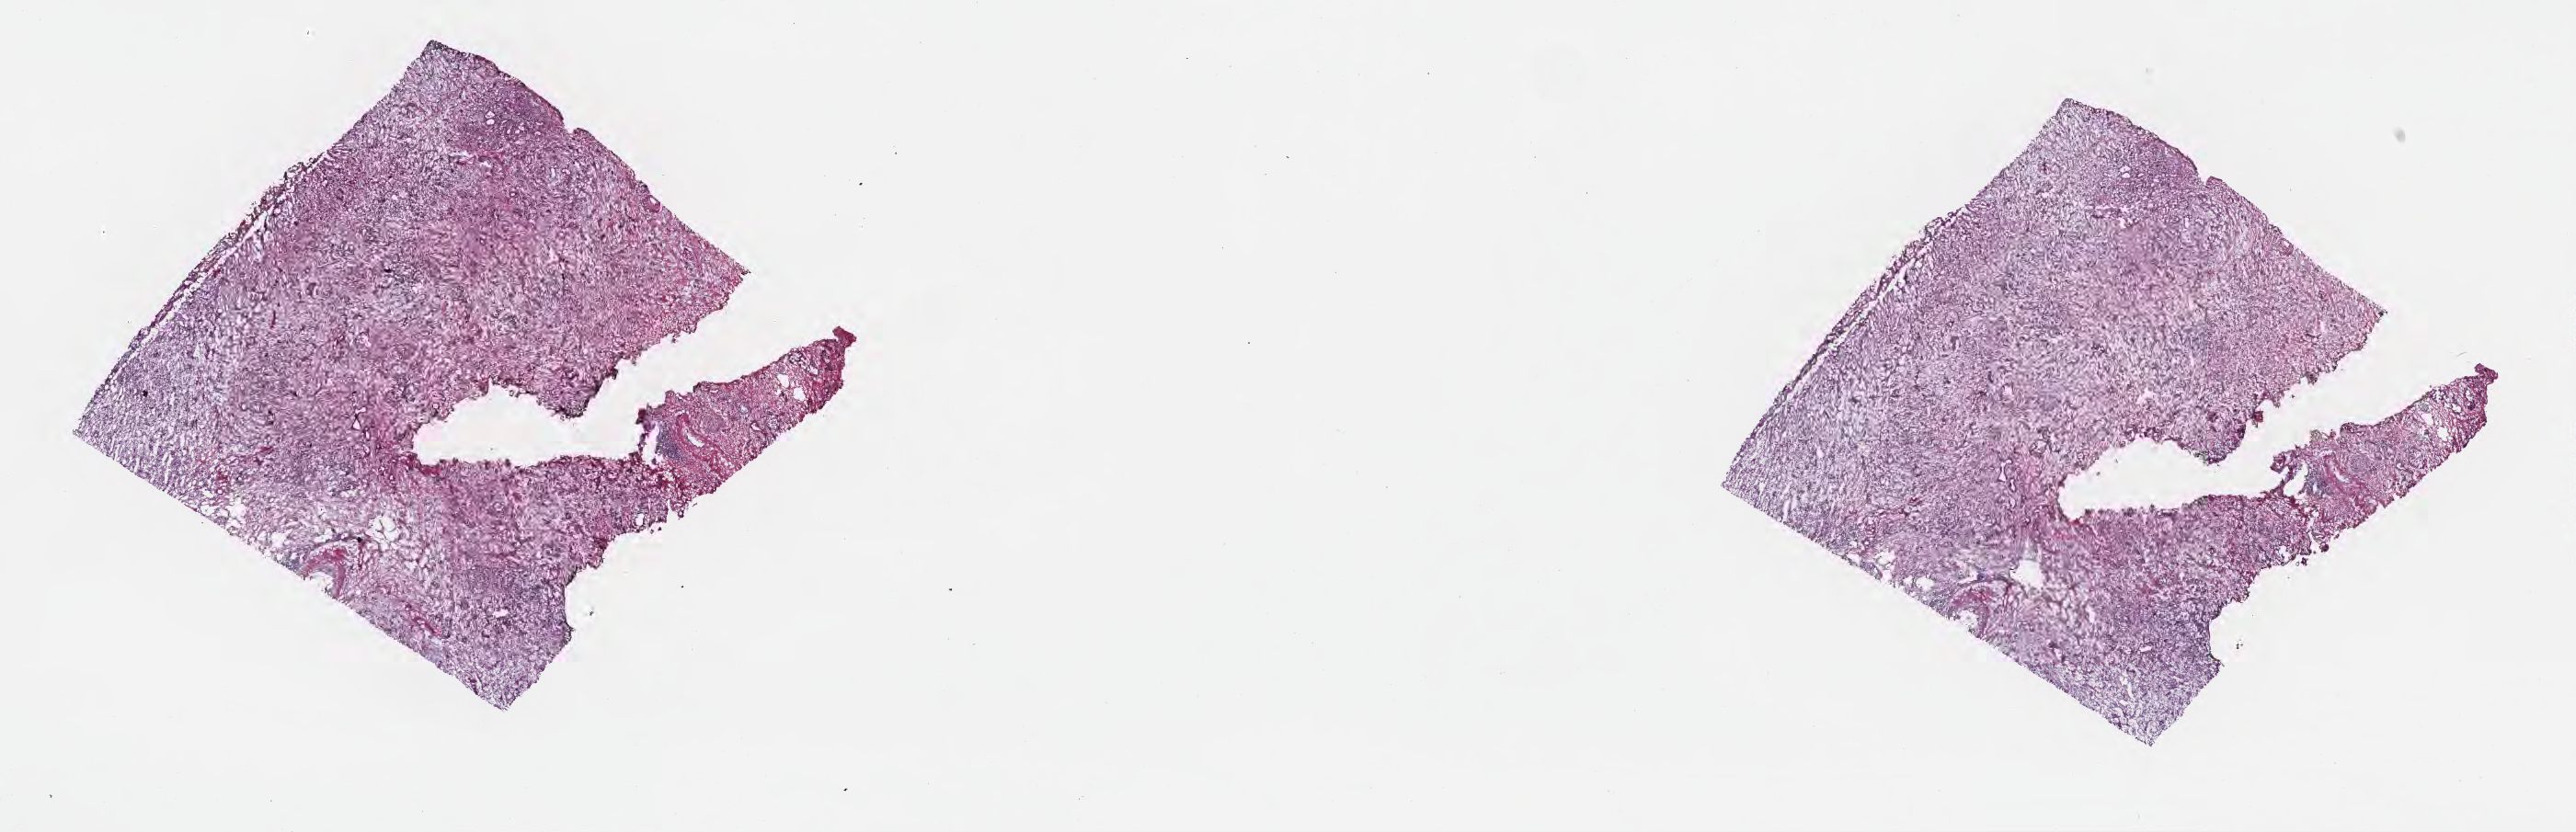
H&E whole-slide image — a low-resolution overview of the entire scanned area, about 22.7 x 7.3 mm, frozen section (tissue freezing medium), primary tumor, site: head of pancreas. Male, age 75 years at initial diagnosis. Tumor grade: G2 (moderately differentiated). Pathologist review of this section (percent, as recorded): tumor cells 15%, tumor nuclei 80%, stromal cells 85%, necrosis 0%, normal cells 0%. Infiltration values recorded for this section: lymphocyte infiltration 0%, monocyte infiltration 0%, neutrophil infiltration 0%.
Histologic diagnosis: Infiltrating duct carcinoma, NOS. AJCC pathologic stage: Stage III. Section: top of the tissue portion.